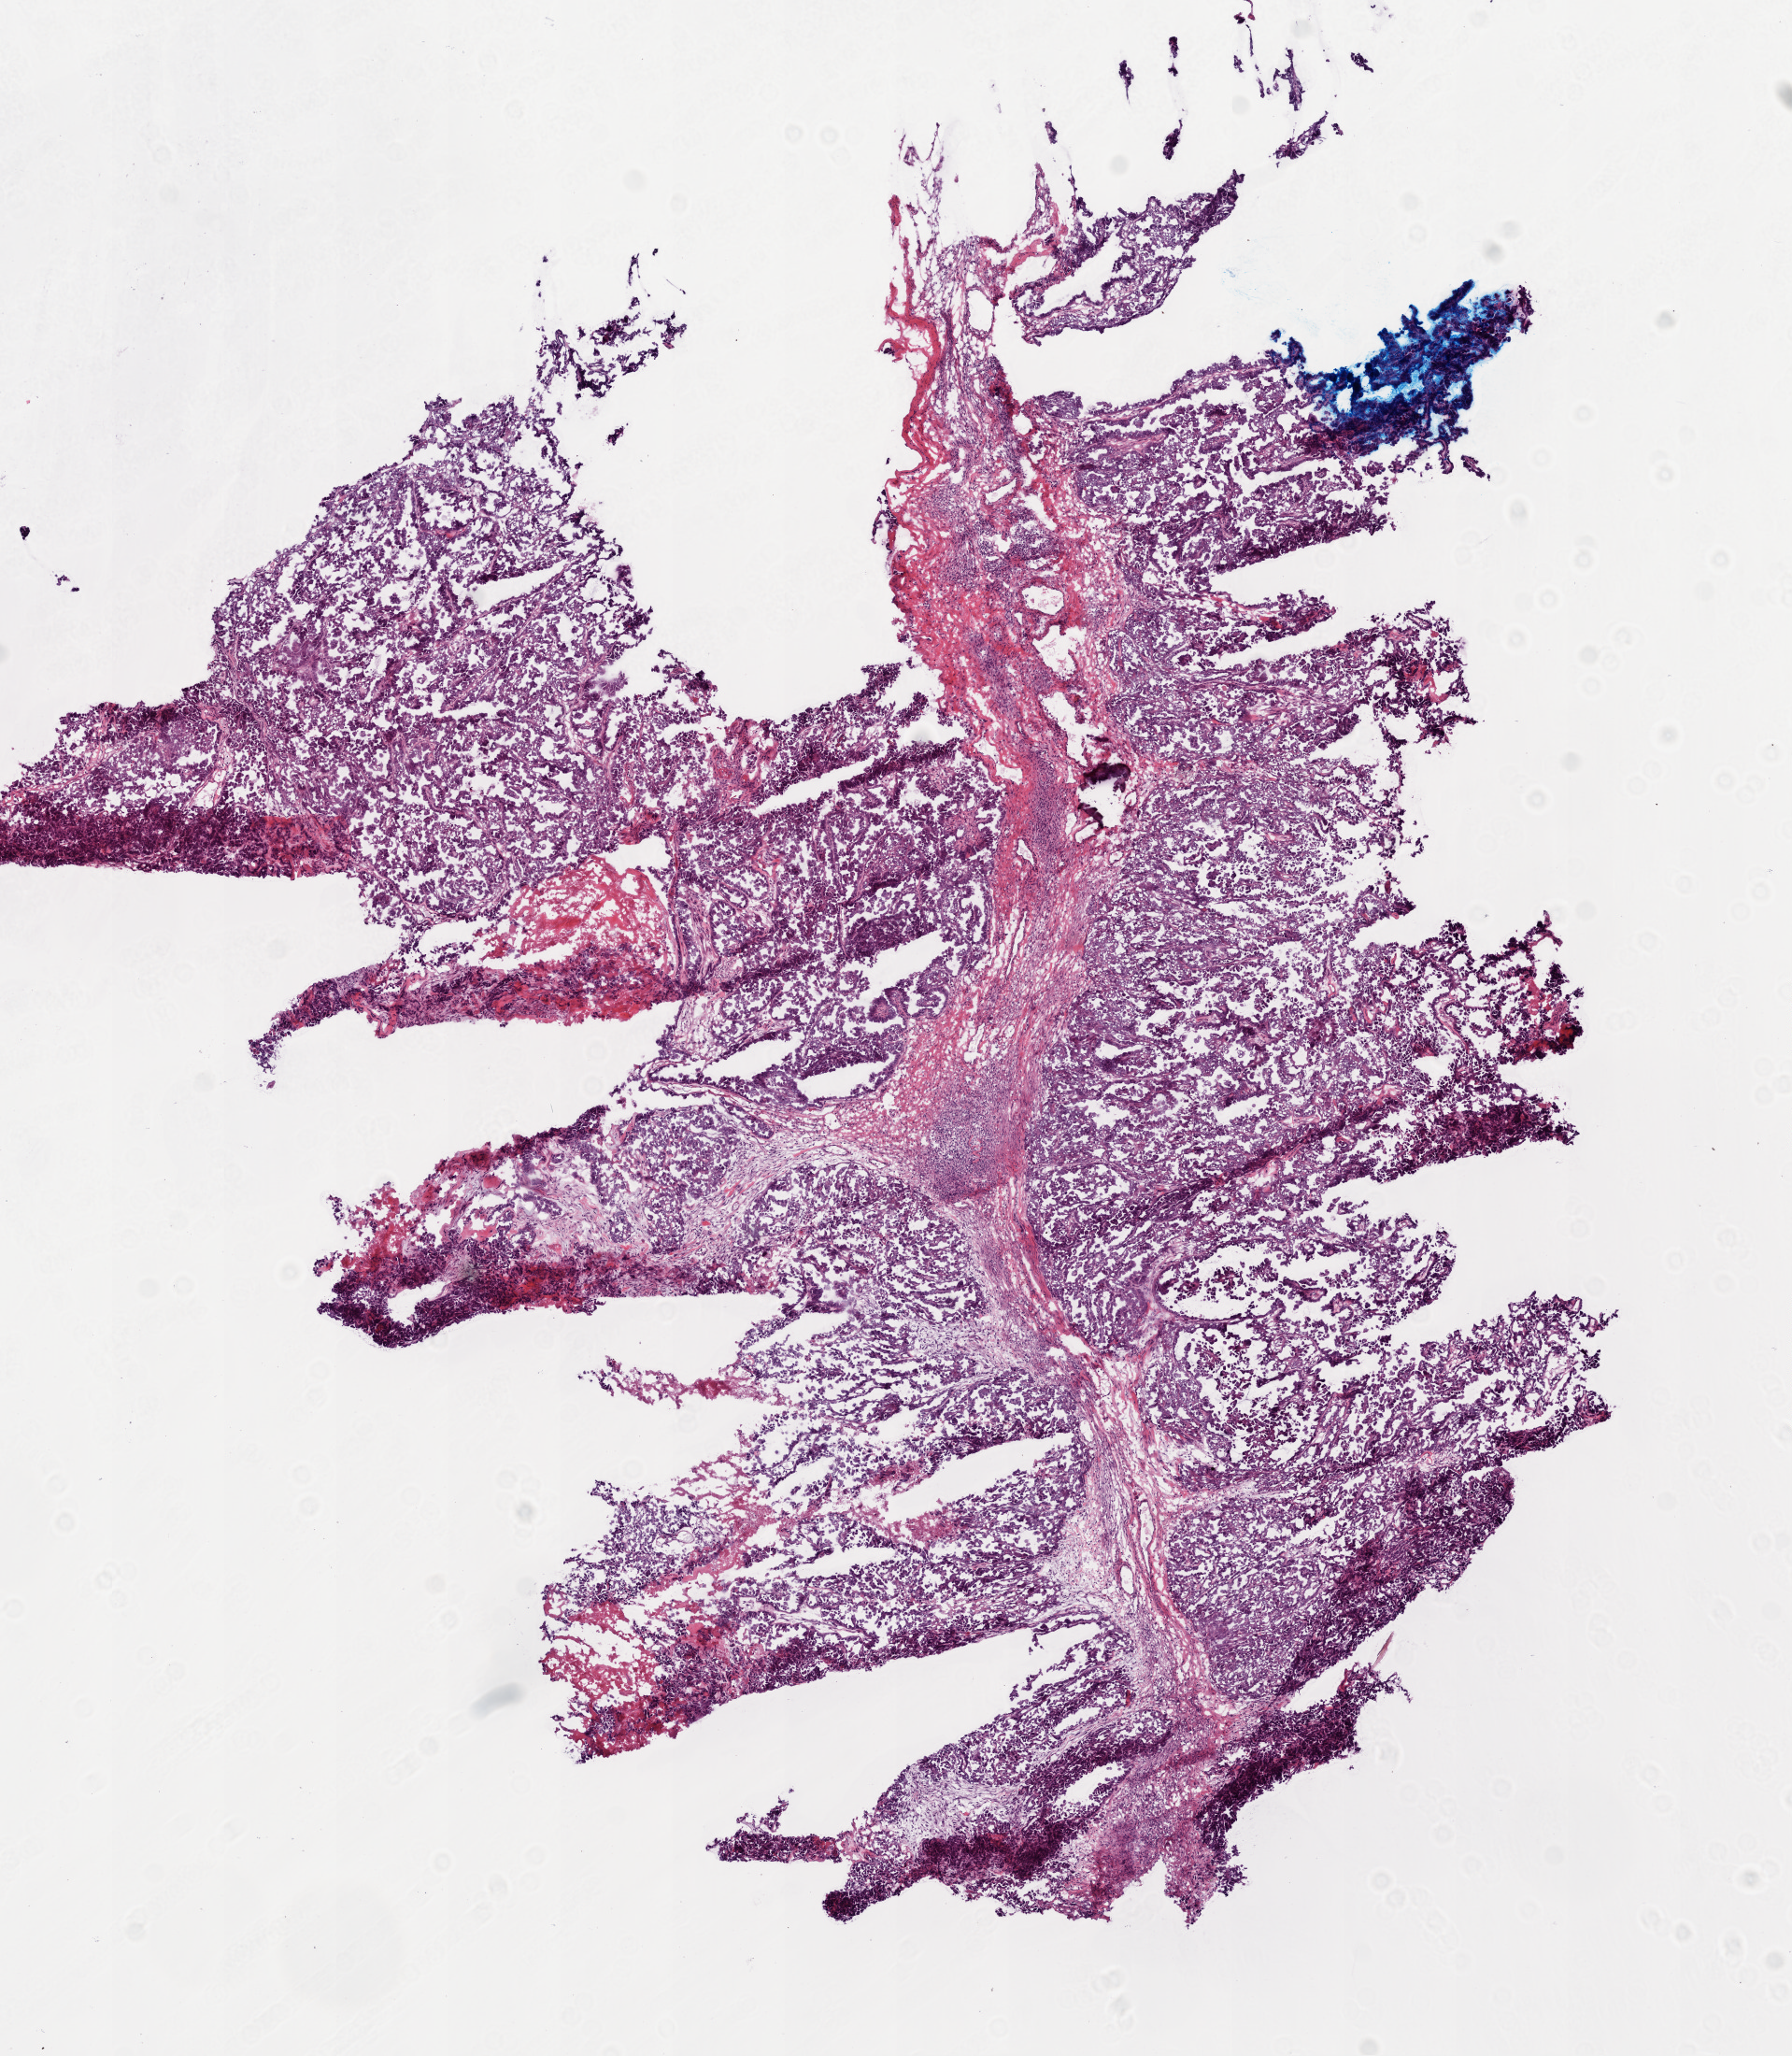
Whole-slide histology image, H&E, whole scanned area (about 7.7 x 8.9 mm, from a 20x scan) shown as a low-resolution overview. Frozen section. Sample: primary tumour, ovary. Female, age 63 years at initial diagnosis.
Pathologic diagnosis: Serous cystadenocarcinoma, NOS.